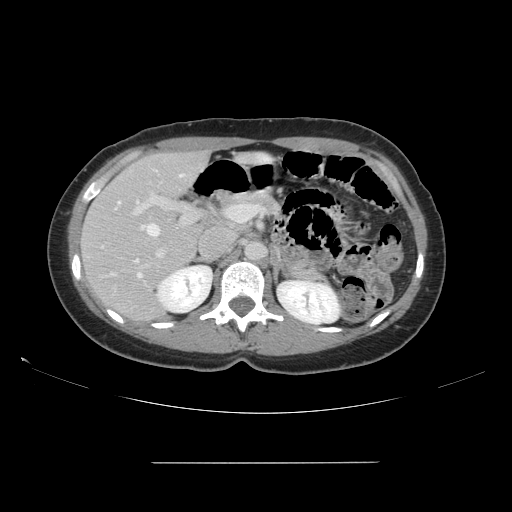
Contrast-enhanced abdominal CT, one axial slice. Position 91 of 151 along the scan axis. Soft-tissue window (W 400 / L 40 HU). 512 × 512 image matrix, field of view 421 × 421 mm. Female patient, age 46 years. From the clinical record (not read from this slice): diagnosis: colorectal cancer liver metastases, imaged before liver resection; multiple liver metastases: yes.
Outlined on this slice (outlined manually by an expert reader):
- hepatic veins: box from (x=112, y=174) to (x=184, y=277) px
- liver: (x=82, y=152)–(x=208, y=322)
- planned liver remnant (the part of the liver to remain after resection): (x=91, y=153)–(x=202, y=272)
- portal vein (with intrahepatic branches): (x=131, y=181)–(x=247, y=270)